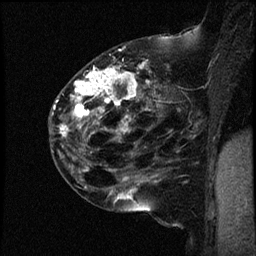
Breast MRI (dynamic contrast-enhanced), one sagittal slice; position 28 of 44 along the scan axis; dynamic contrast-enhanced study with each time point stored as its own series, time point 2 of 4 at this slice position (early post-contrast, ordered by acquisition time); 1.5 T; TE 4.2 ms, TR 17.7 ms; 2 mm slice thickness; 256 × 256 image matrix, field of view 200 × 200 mm. Female patient, age 52 years. From the clinical record (not read from this slice): setting: breast cancer imaged before/during neoadjuvant chemotherapy; receptor status: HR-positive, HER2-negative.
Outlined on this slice (semi-automatically segmented with operator editing):
- analysis volume of interest (the breast-tissue region the enhancement analysis was run in; not a lesion): bounding box <49,48,163,147> (left, top, right, bottom; pixels)
- tumour enhancement mask (voxels above the 100 % enhancement threshold inside the analysis volume of interest): <59,67,147,142>